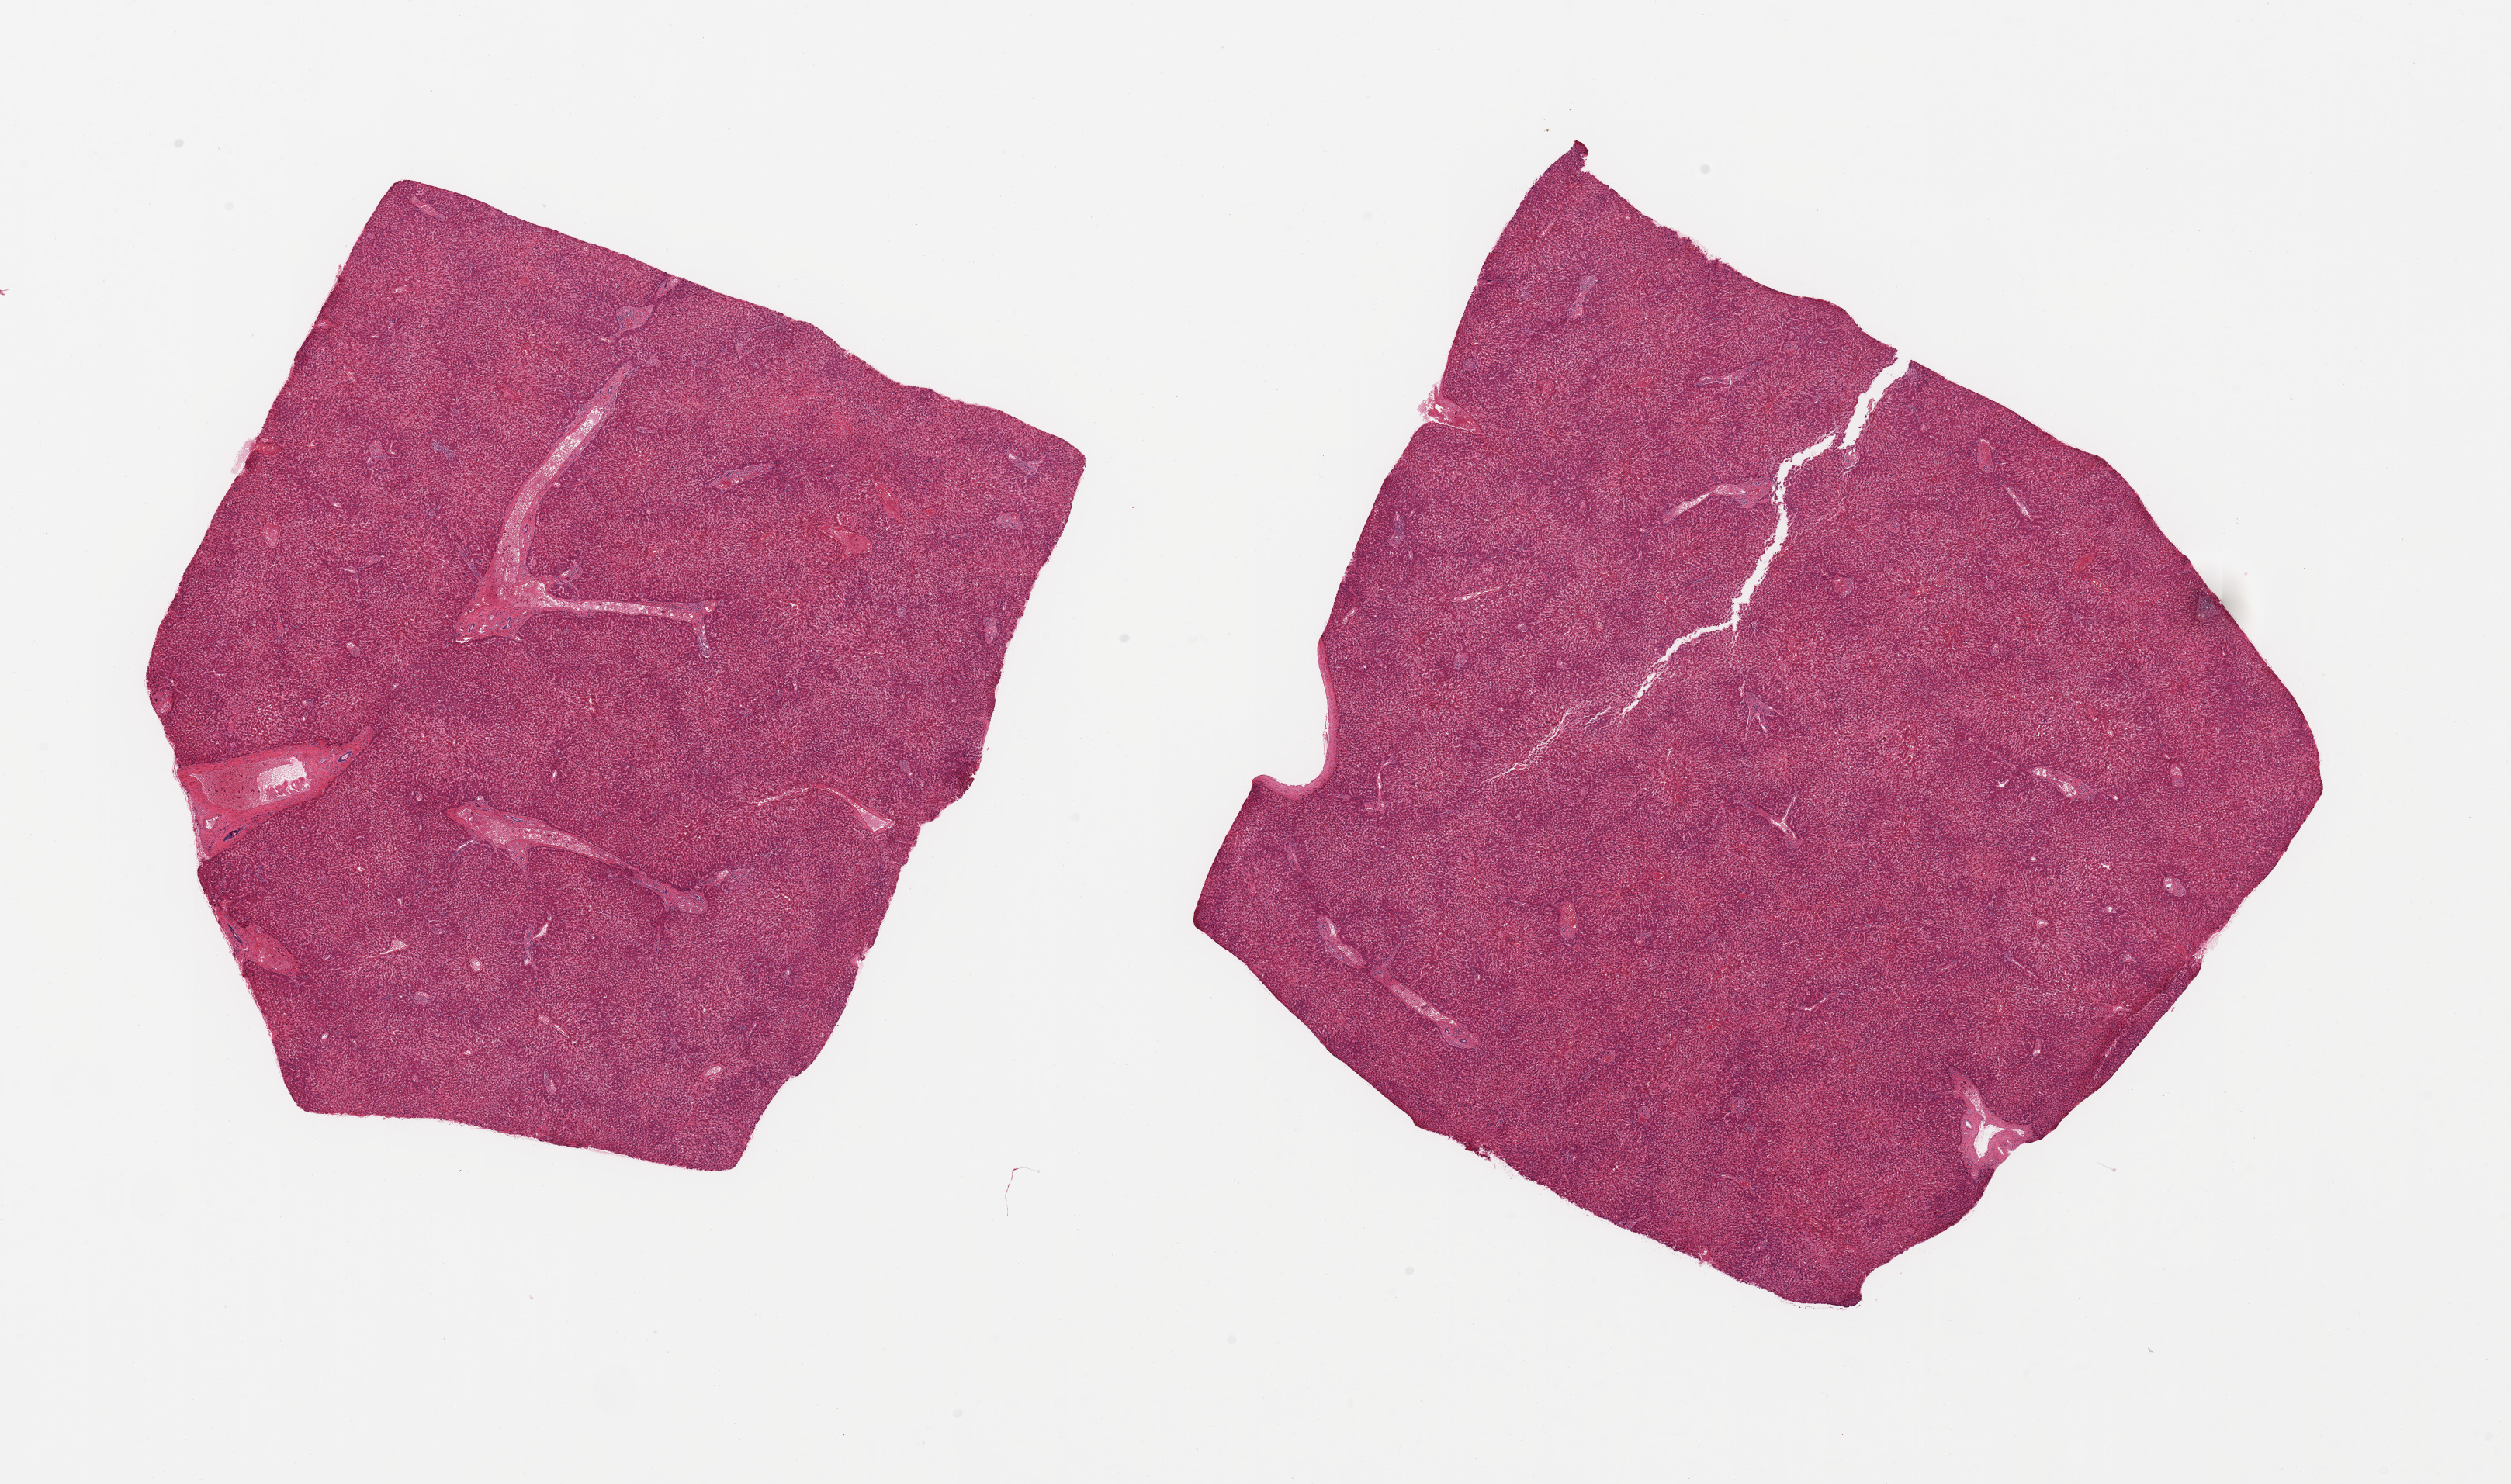
Digitized H&E-stained section — whole scanned area (about 25.6 x 15.1 mm, acquisition: 20x scan) shown as a low-resolution overview, PAXgene-fixed, paraffin-embedded tissue, sampled site (target tissue): liver, donor tissue sample. Donor sex: male.
Review note (as recorded): 2 pieces; minimal congestion; no inflammation.